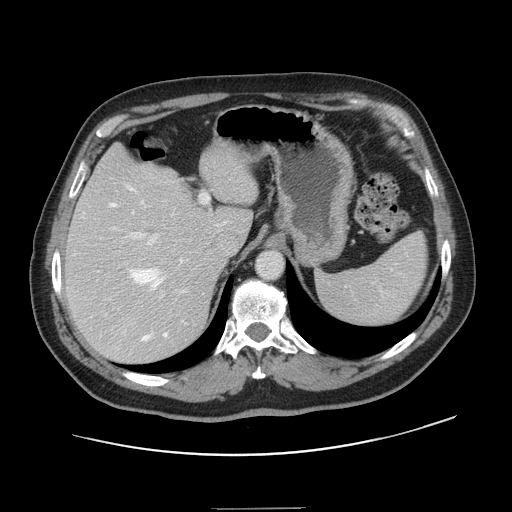
Contrast-enhanced abdominal CT, one axial slice; slice 101 of 143 in the series (ordered by position); intravenous contrast given; soft-tissue window (W 400 / L 40 HU); 2.5 mm slice thickness; 512 × 512 image matrix, field of view 402 × 402 mm. Male patient, age 62 years. Case-level facts recorded for this patient, not image findings: diagnosis: colorectal cancer liver metastases, imaged before liver resection; multiple liver metastases: yes; largest metastasis: 2.7 cm; disease in both lobes: no.
Outlined on this slice (expert manual segmentation):
- hepatic veins: bounding box <109,187,187,341> (left, top, right, bottom; pixels)
- liver: <66,147,257,363>
- planned liver remnant (the part of the liver to remain after resection): <66,146,256,264>
- portal vein (with intrahepatic branches): <114,194,209,292>